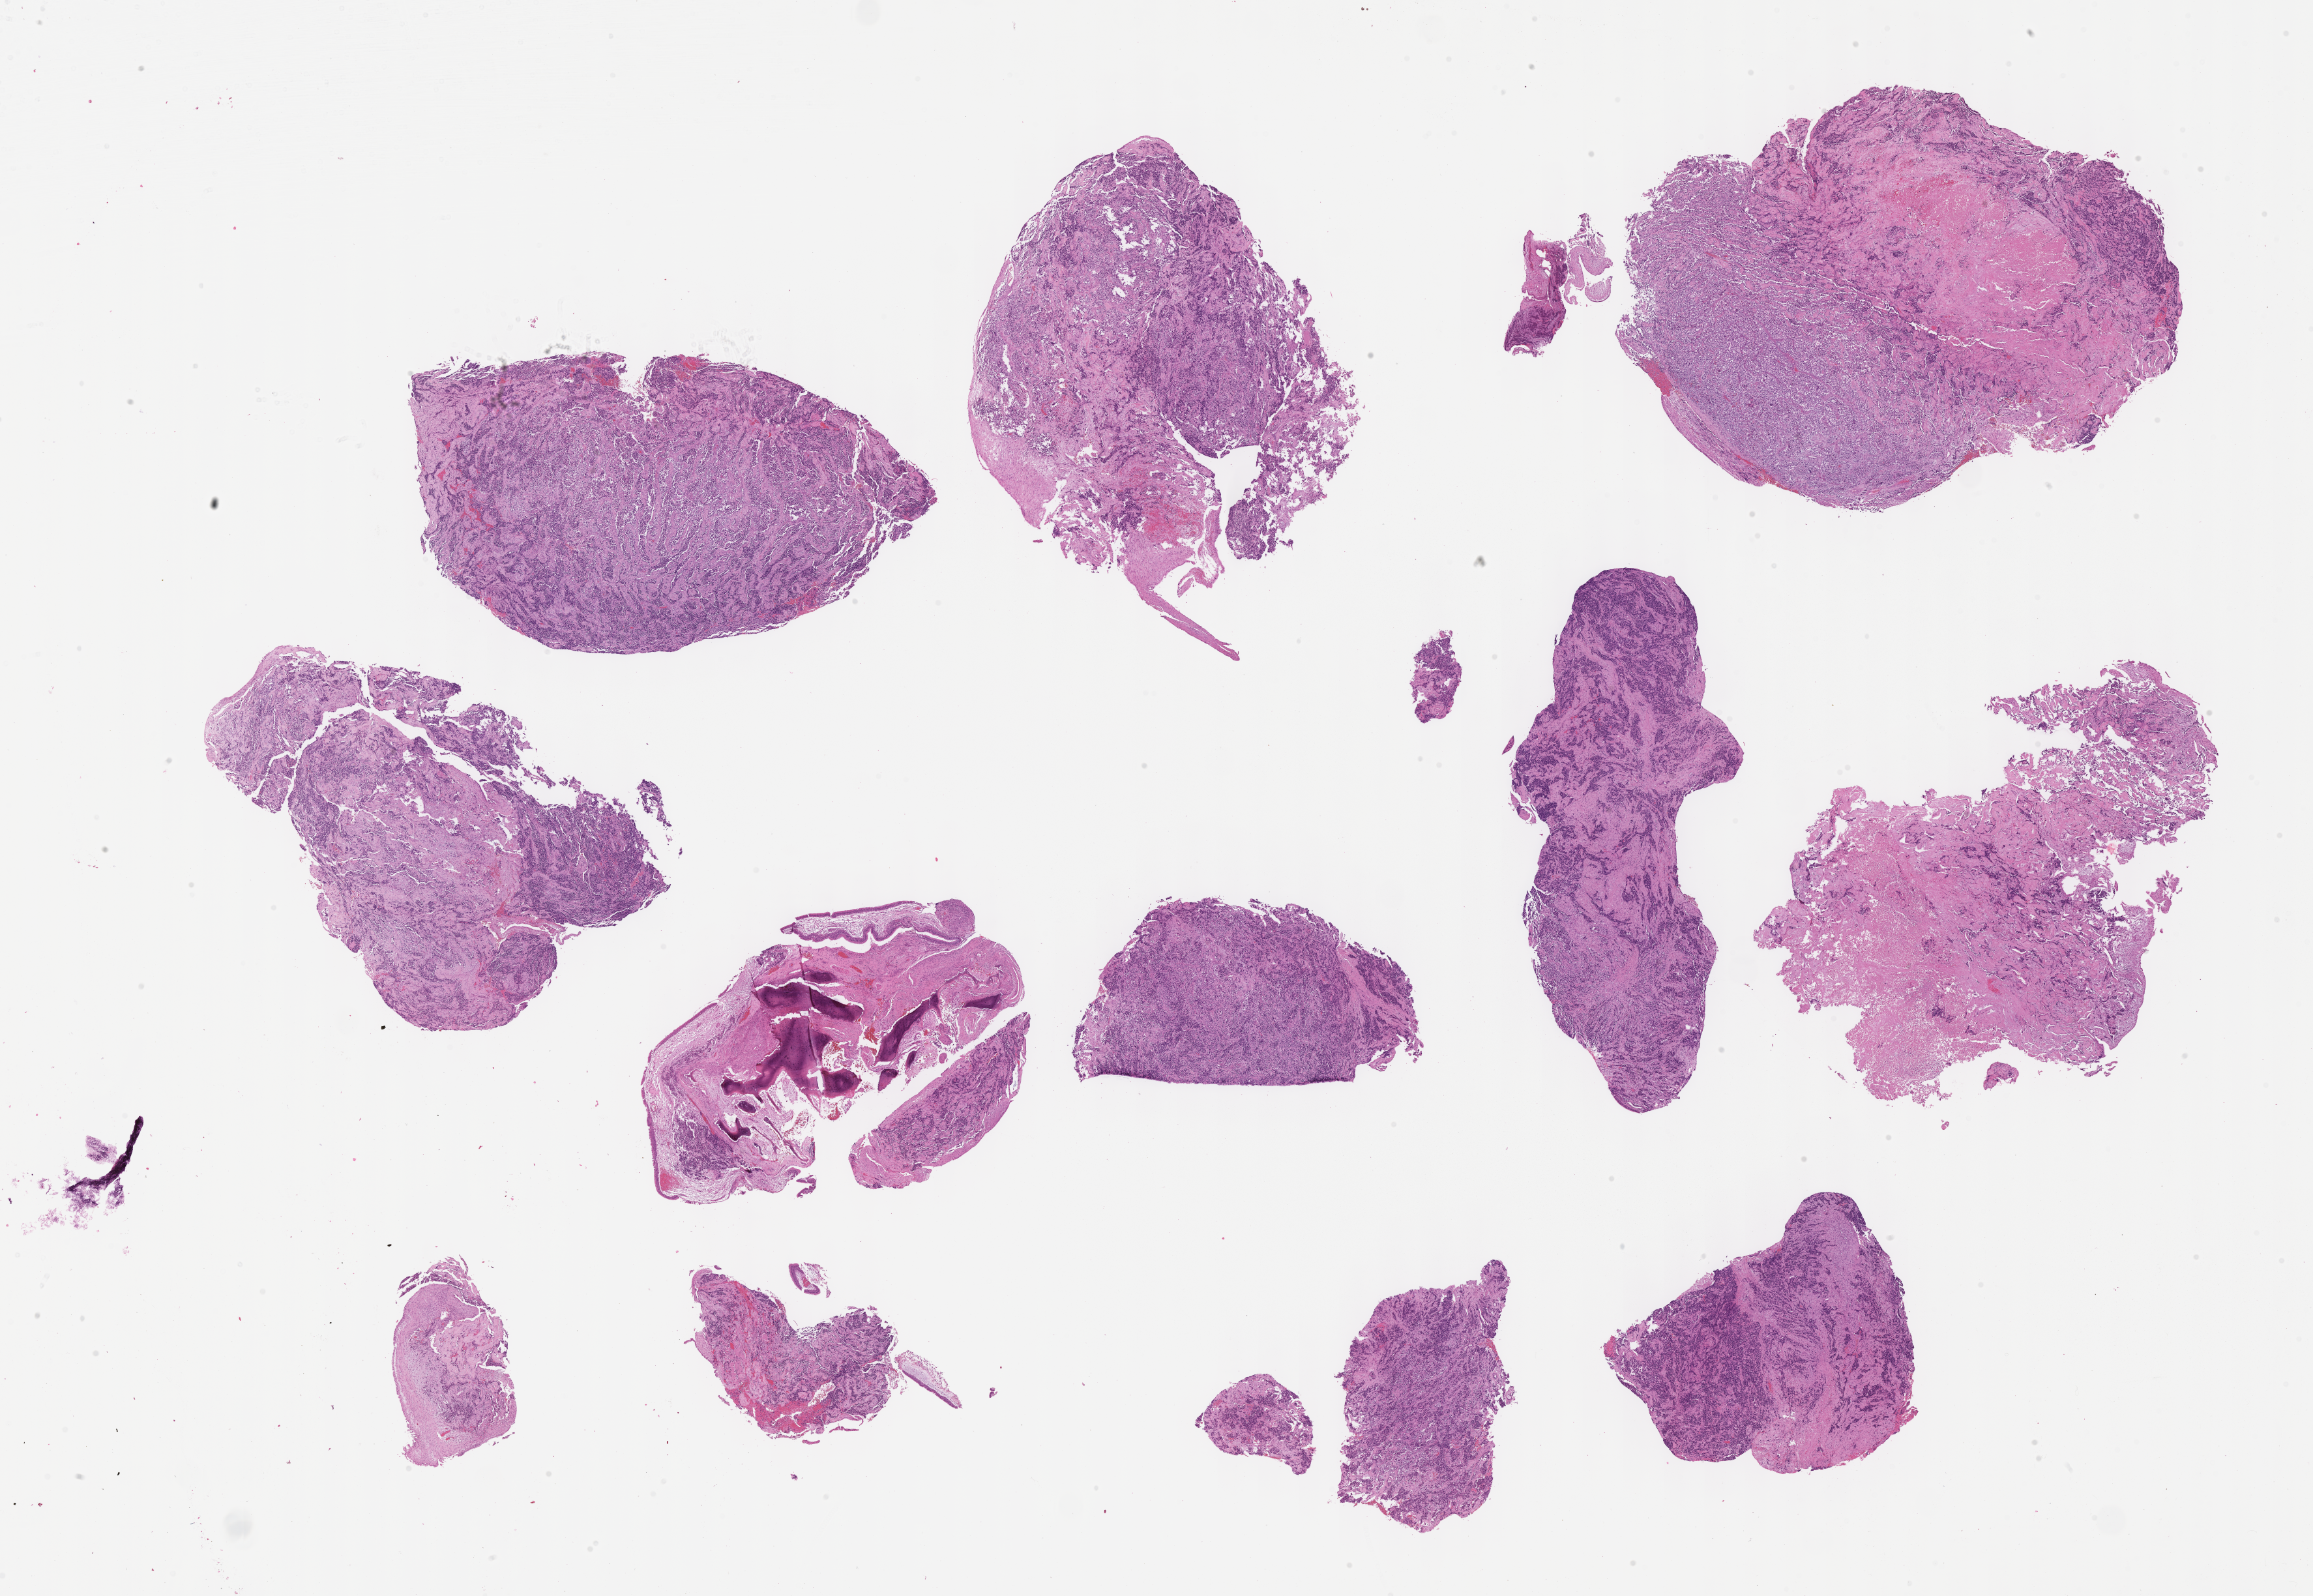
Hematoxylin and eosin (H&E) whole-slide image of tumor tissue, low-resolution overview of the scanned area, about 28.7 x 19.8 mm, formalin-fixed, paraffin-embedded (FFPE) tissue, sample anatomic site: maxillary sinus. Patient: male, age 15.2 years at diagnosis.
- stage (as recorded): 3
- diagnosis: rhabdomyosarcoma; histological classification: alveolar rhabdomyosarcoma
- metastatic status at presentation (as recorded): non-metastatic
- primary site (case record): paranasal Sinus